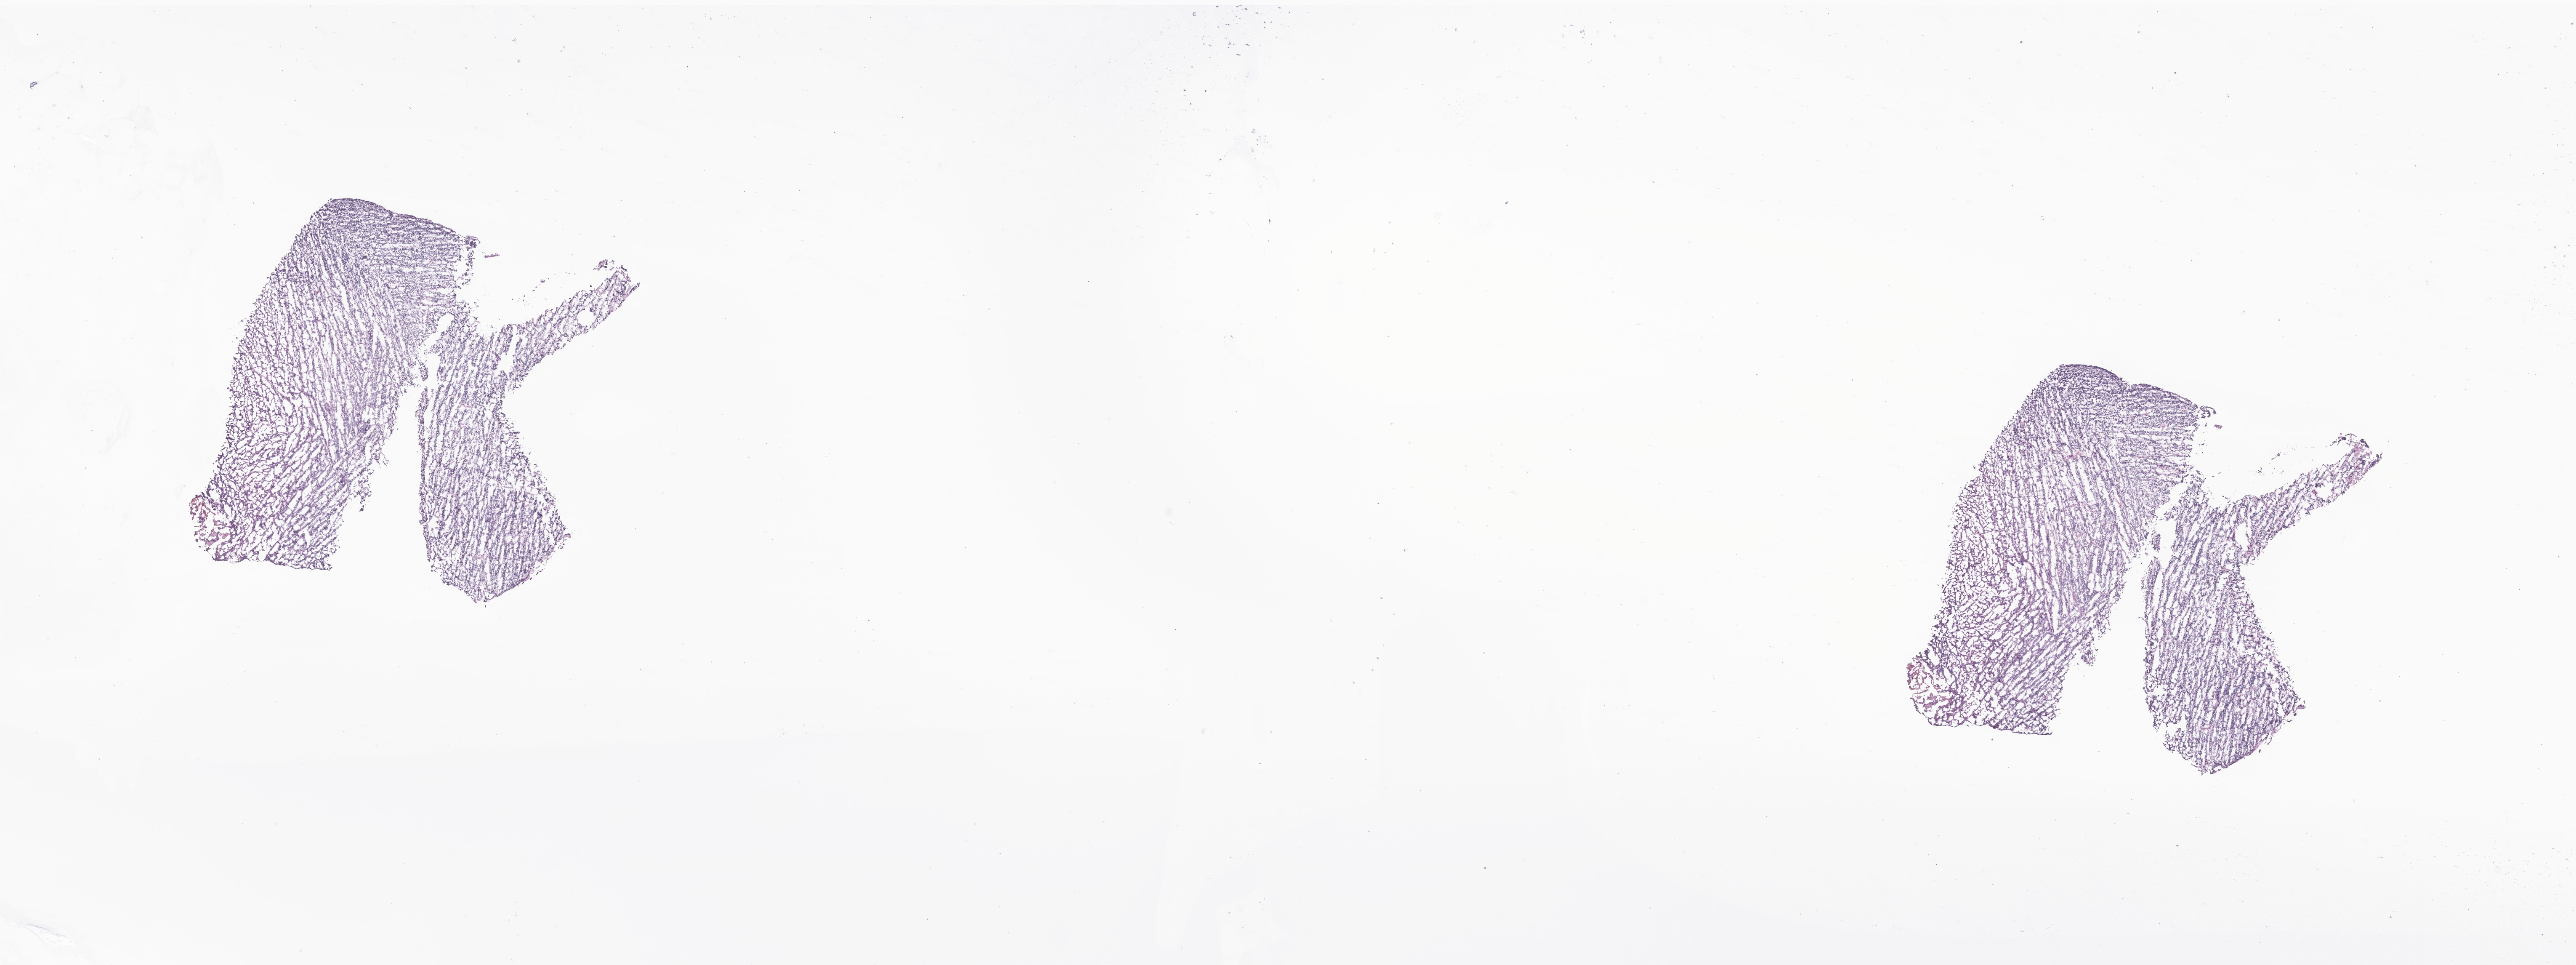
H&E whole-slide image of tumor tissue from the brain — a low-resolution overview of the entire scanned area, about 25.8 x 9.7 mm, frozen section. Patient: female, age 181 months (15 years 1 month).
Recorded diagnosis: Medulloblastoma, NOS.